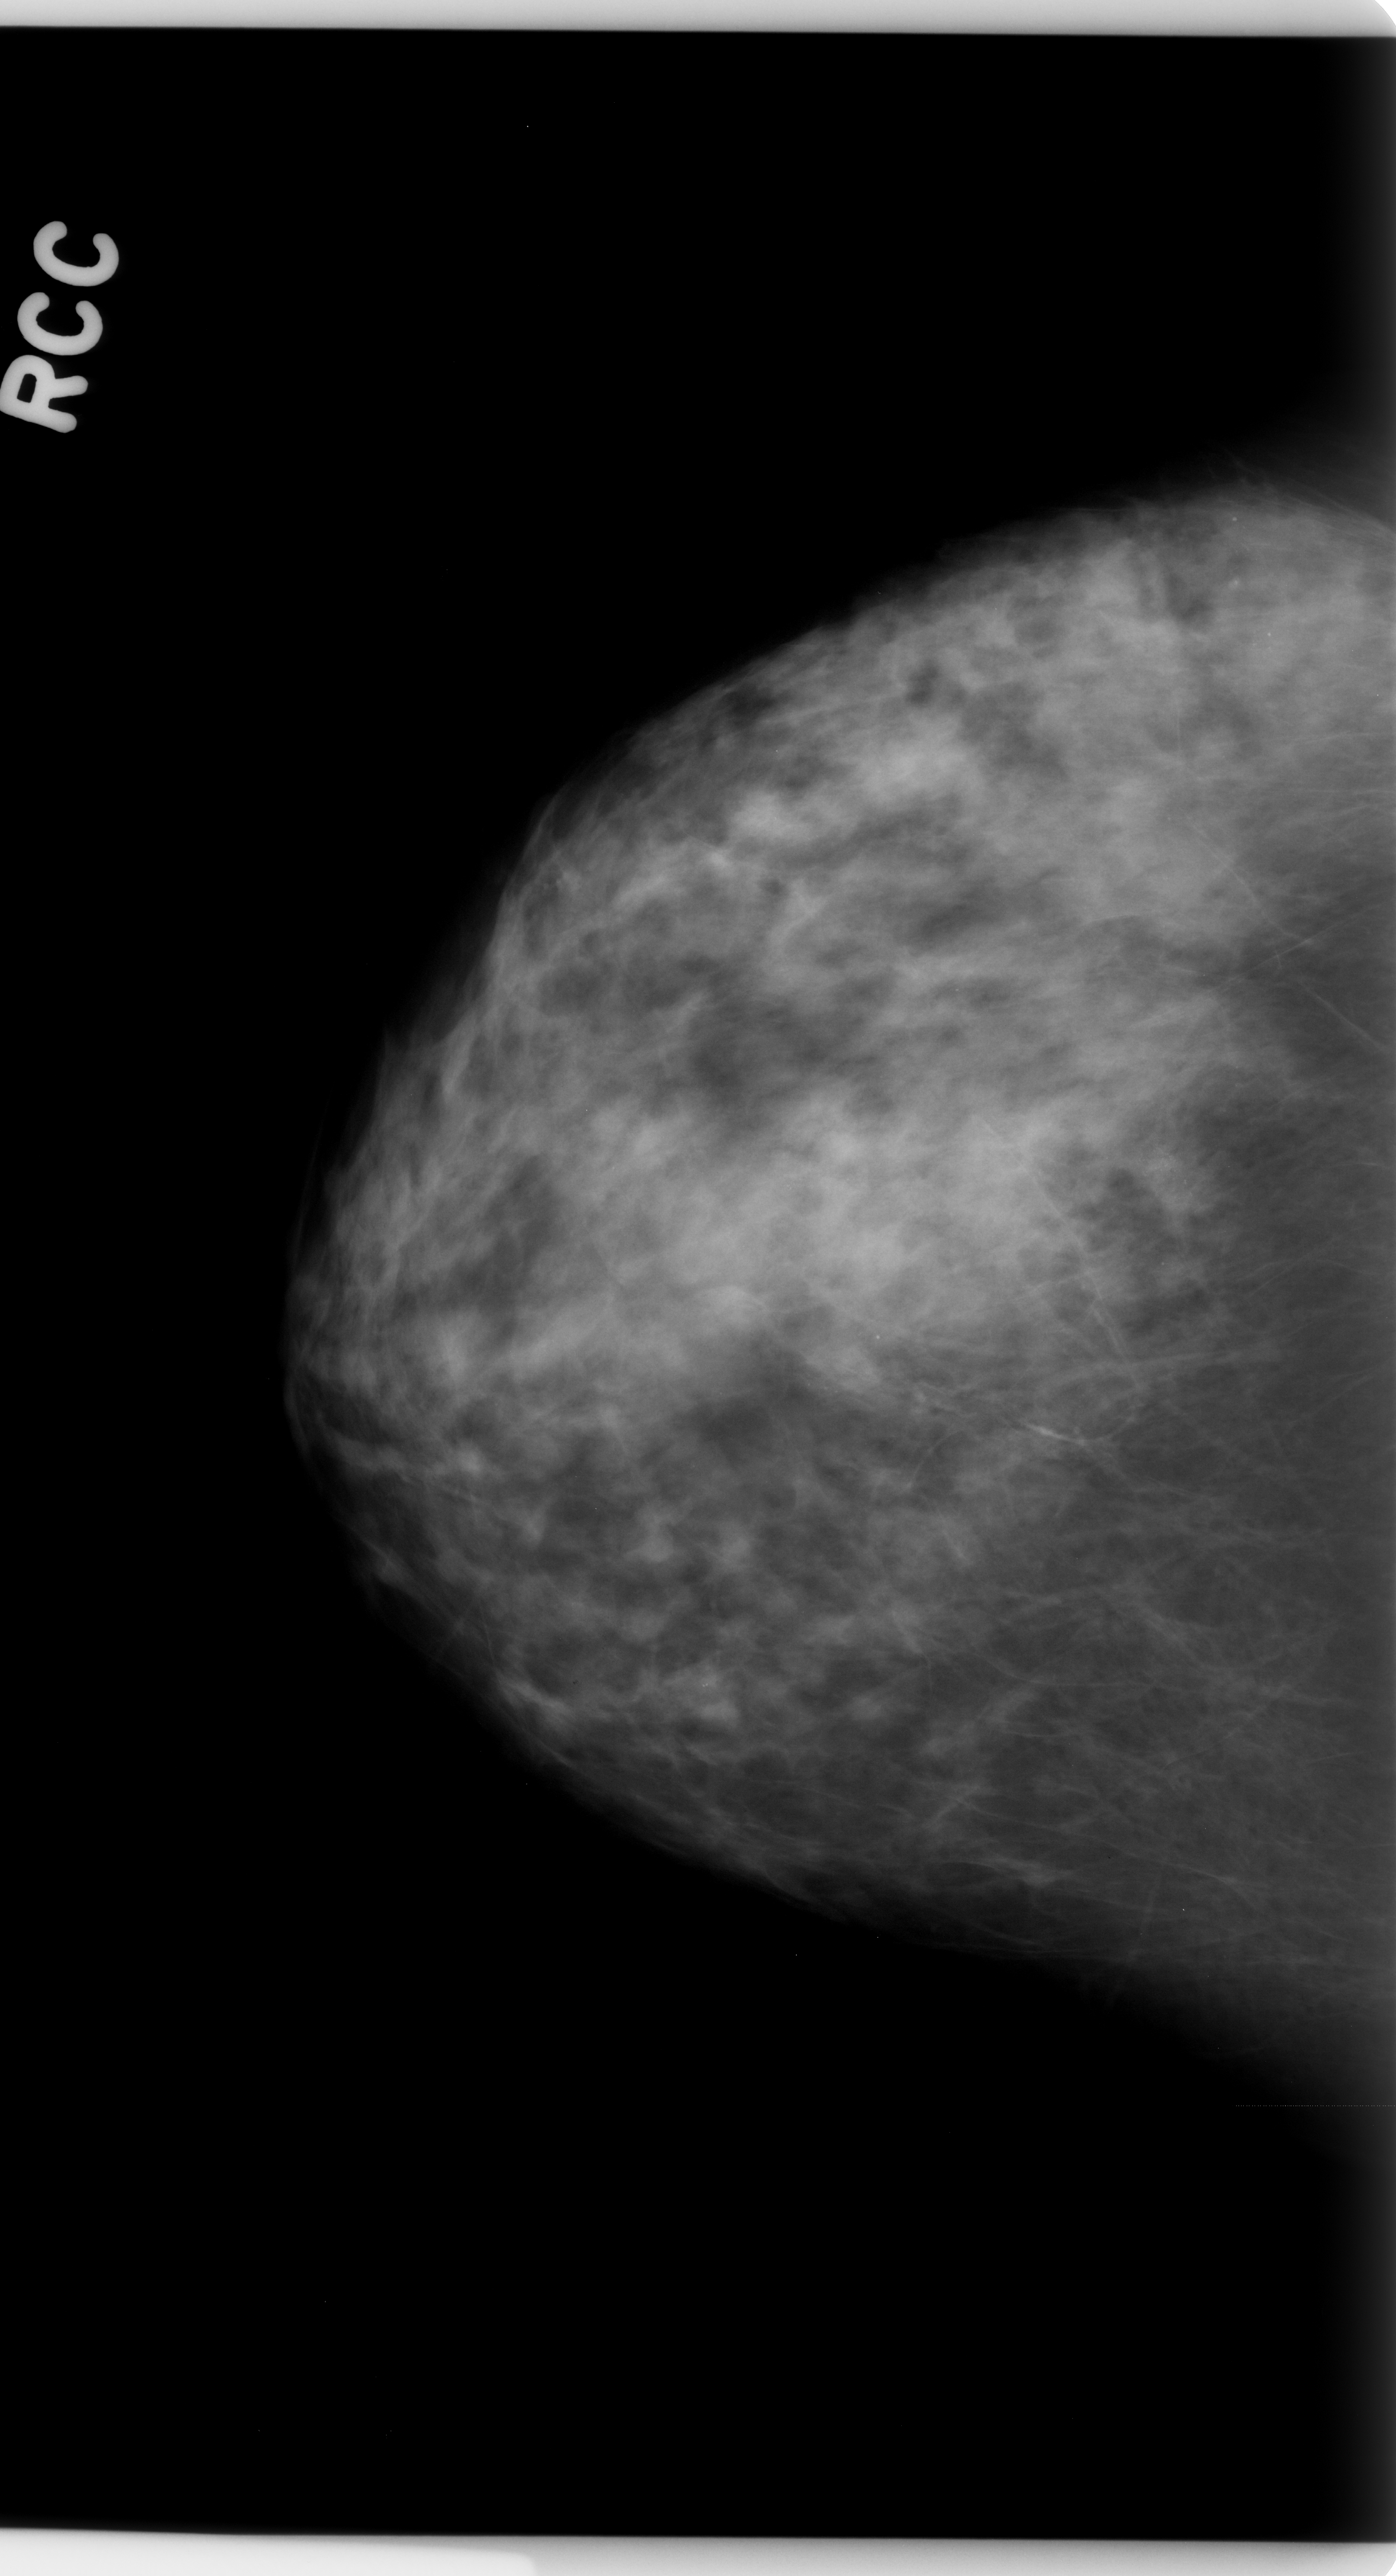
Digitized screen-film mammogram; right breast; craniocaudal (CC) view; BI-RADS breast density category 3 (scale 1–4); 1396 × 2576 image matrix.
Expert-marked regions of interest on this image (one box per marked abnormality):
- calcifications, morphology amorphous, distribution clustered; BI-RADS assessment category 4; pathology (as recorded): benign: box from (x=1044, y=1093) to (x=1265, y=1282) px